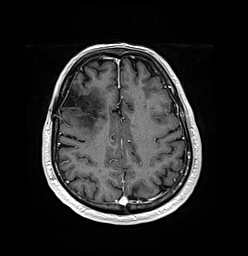
Brain MRI from a brain-tumour surgery series, one axial slice. Position 51 of 176 along the scan axis. T1-weighted post-contrast. 1 mm slice thickness. 248 × 256 image matrix, field of view 242 × 250 mm. From the clinical record (not read from this slice): histopathology: Oligodendroglioma; WHO grade: 3; IDH mutation: yes.
Structures marked on this image (expert manual segmentation):
- previous resection cavity: box from (x=63, y=88) to (x=84, y=108) px